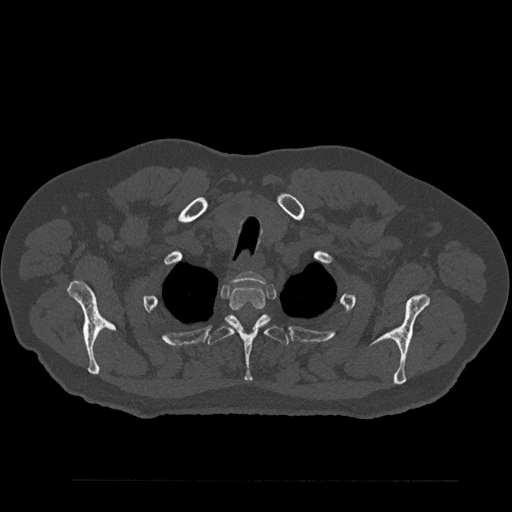
CT including the spine, one axial slice. Position 704 of 797 along the scan axis. 120 kVp. Bone window (W 1800 / L 400 HU). 0.5 mm slice thickness. 512 × 512 image matrix, field of view 430 × 430 mm. Patient: male, 61 years. Case-level facts recorded for this patient, not image findings: primary cancer: prostate.
Structures marked on this image (semi-automatically segmented with operator editing):
- T1 vertebra: bounding box (x1, y1, x2, y2) in pixels: (234, 271, 266, 284)
- T2 vertebra: (229, 285, 265, 311)
- T3 vertebra: (208, 314, 289, 382)